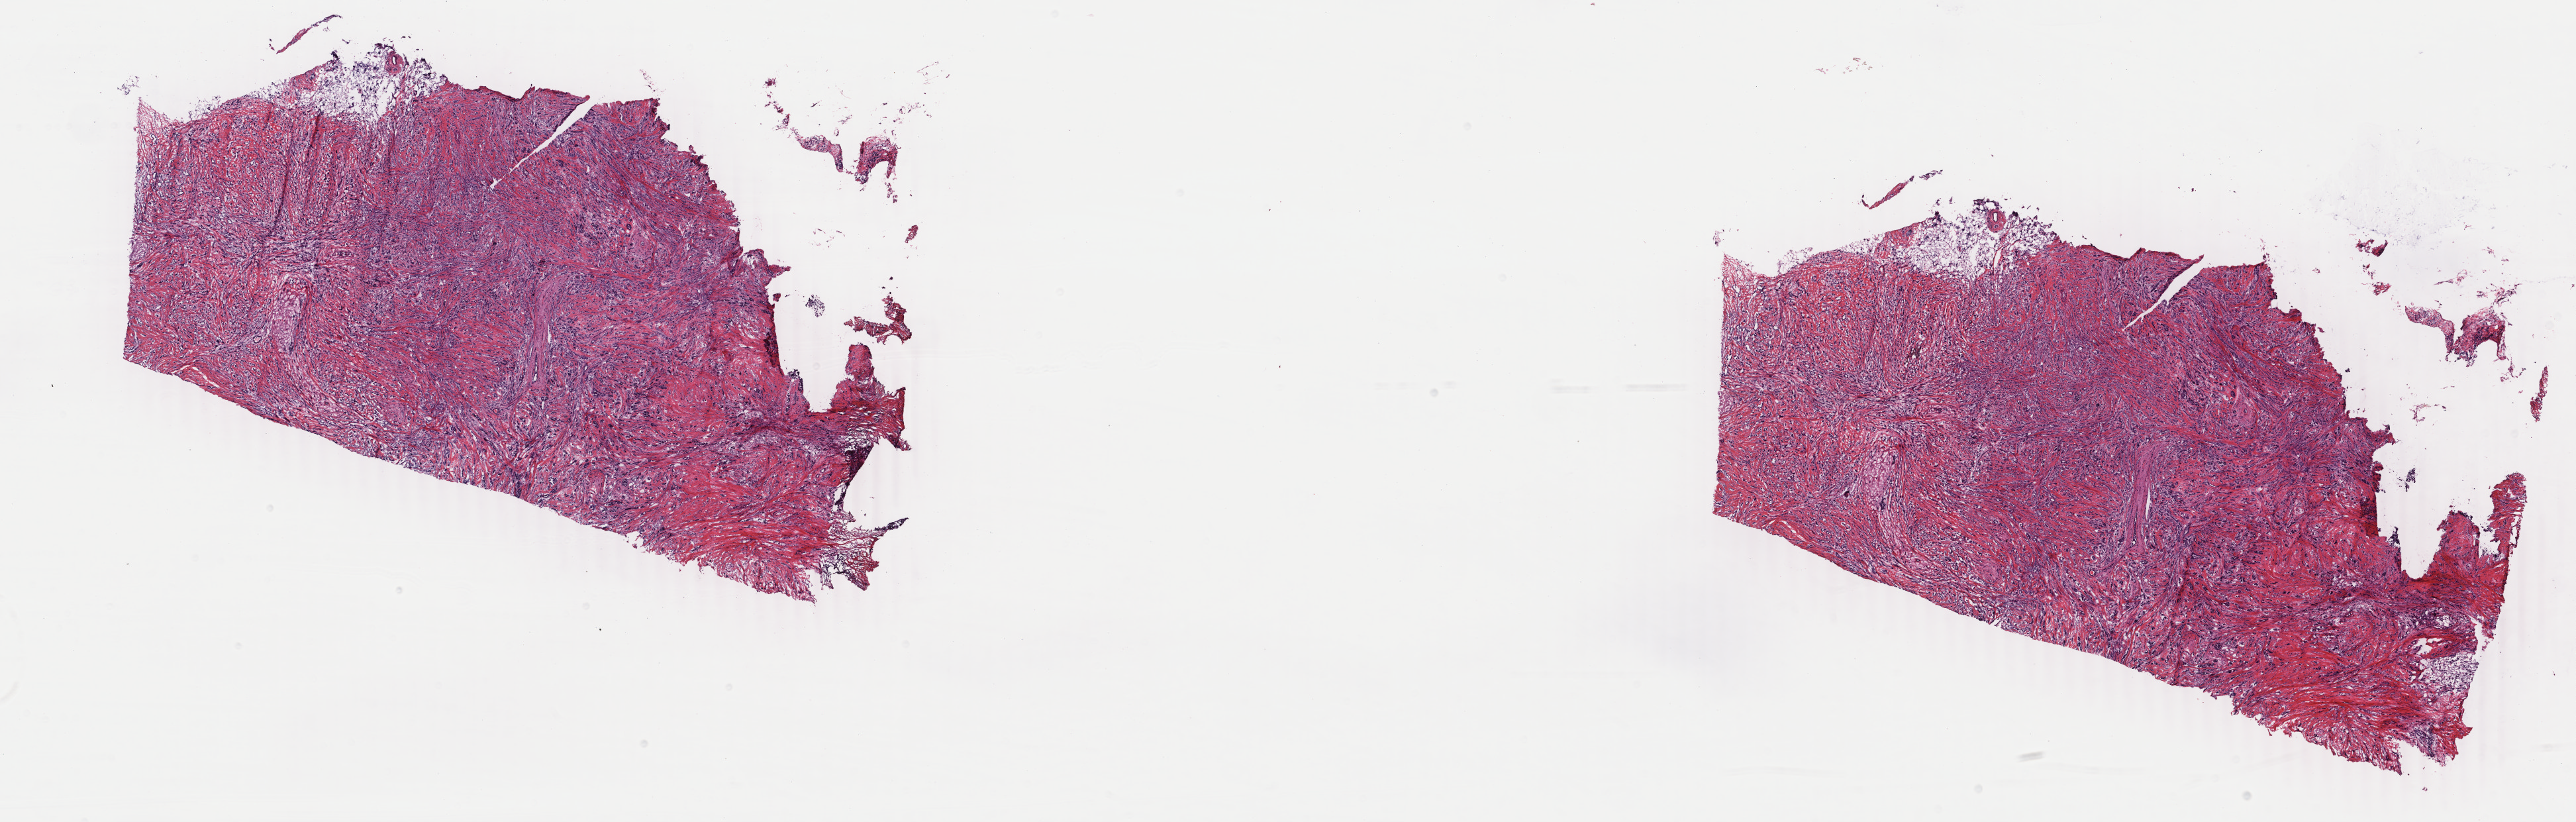
Hematoxylin and eosin (H&E) stained whole-slide image — whole scanned area (about 30.9 x 9.9 mm) shown as a low-resolution overview, frozen section from the bottom of the tissue portion, primary tumour sample from the breast. Female, age 48 years at initial diagnosis. Pathologist review of this section (percent, as recorded): tumour cells 85%, tumour nuclei 85%, normal cells 1%, stromal cells 14%, necrosis 0%. Infiltration values recorded for this section: lymphocyte infiltration 1%, monocyte infiltration 0%, neutrophil infiltration 0%.
• diagnosis: Infiltrating duct mixed with other types of carcinoma
• AJCC pathologic stage: IV
• lymph nodes positive (case pathology): 2 of 2 examined